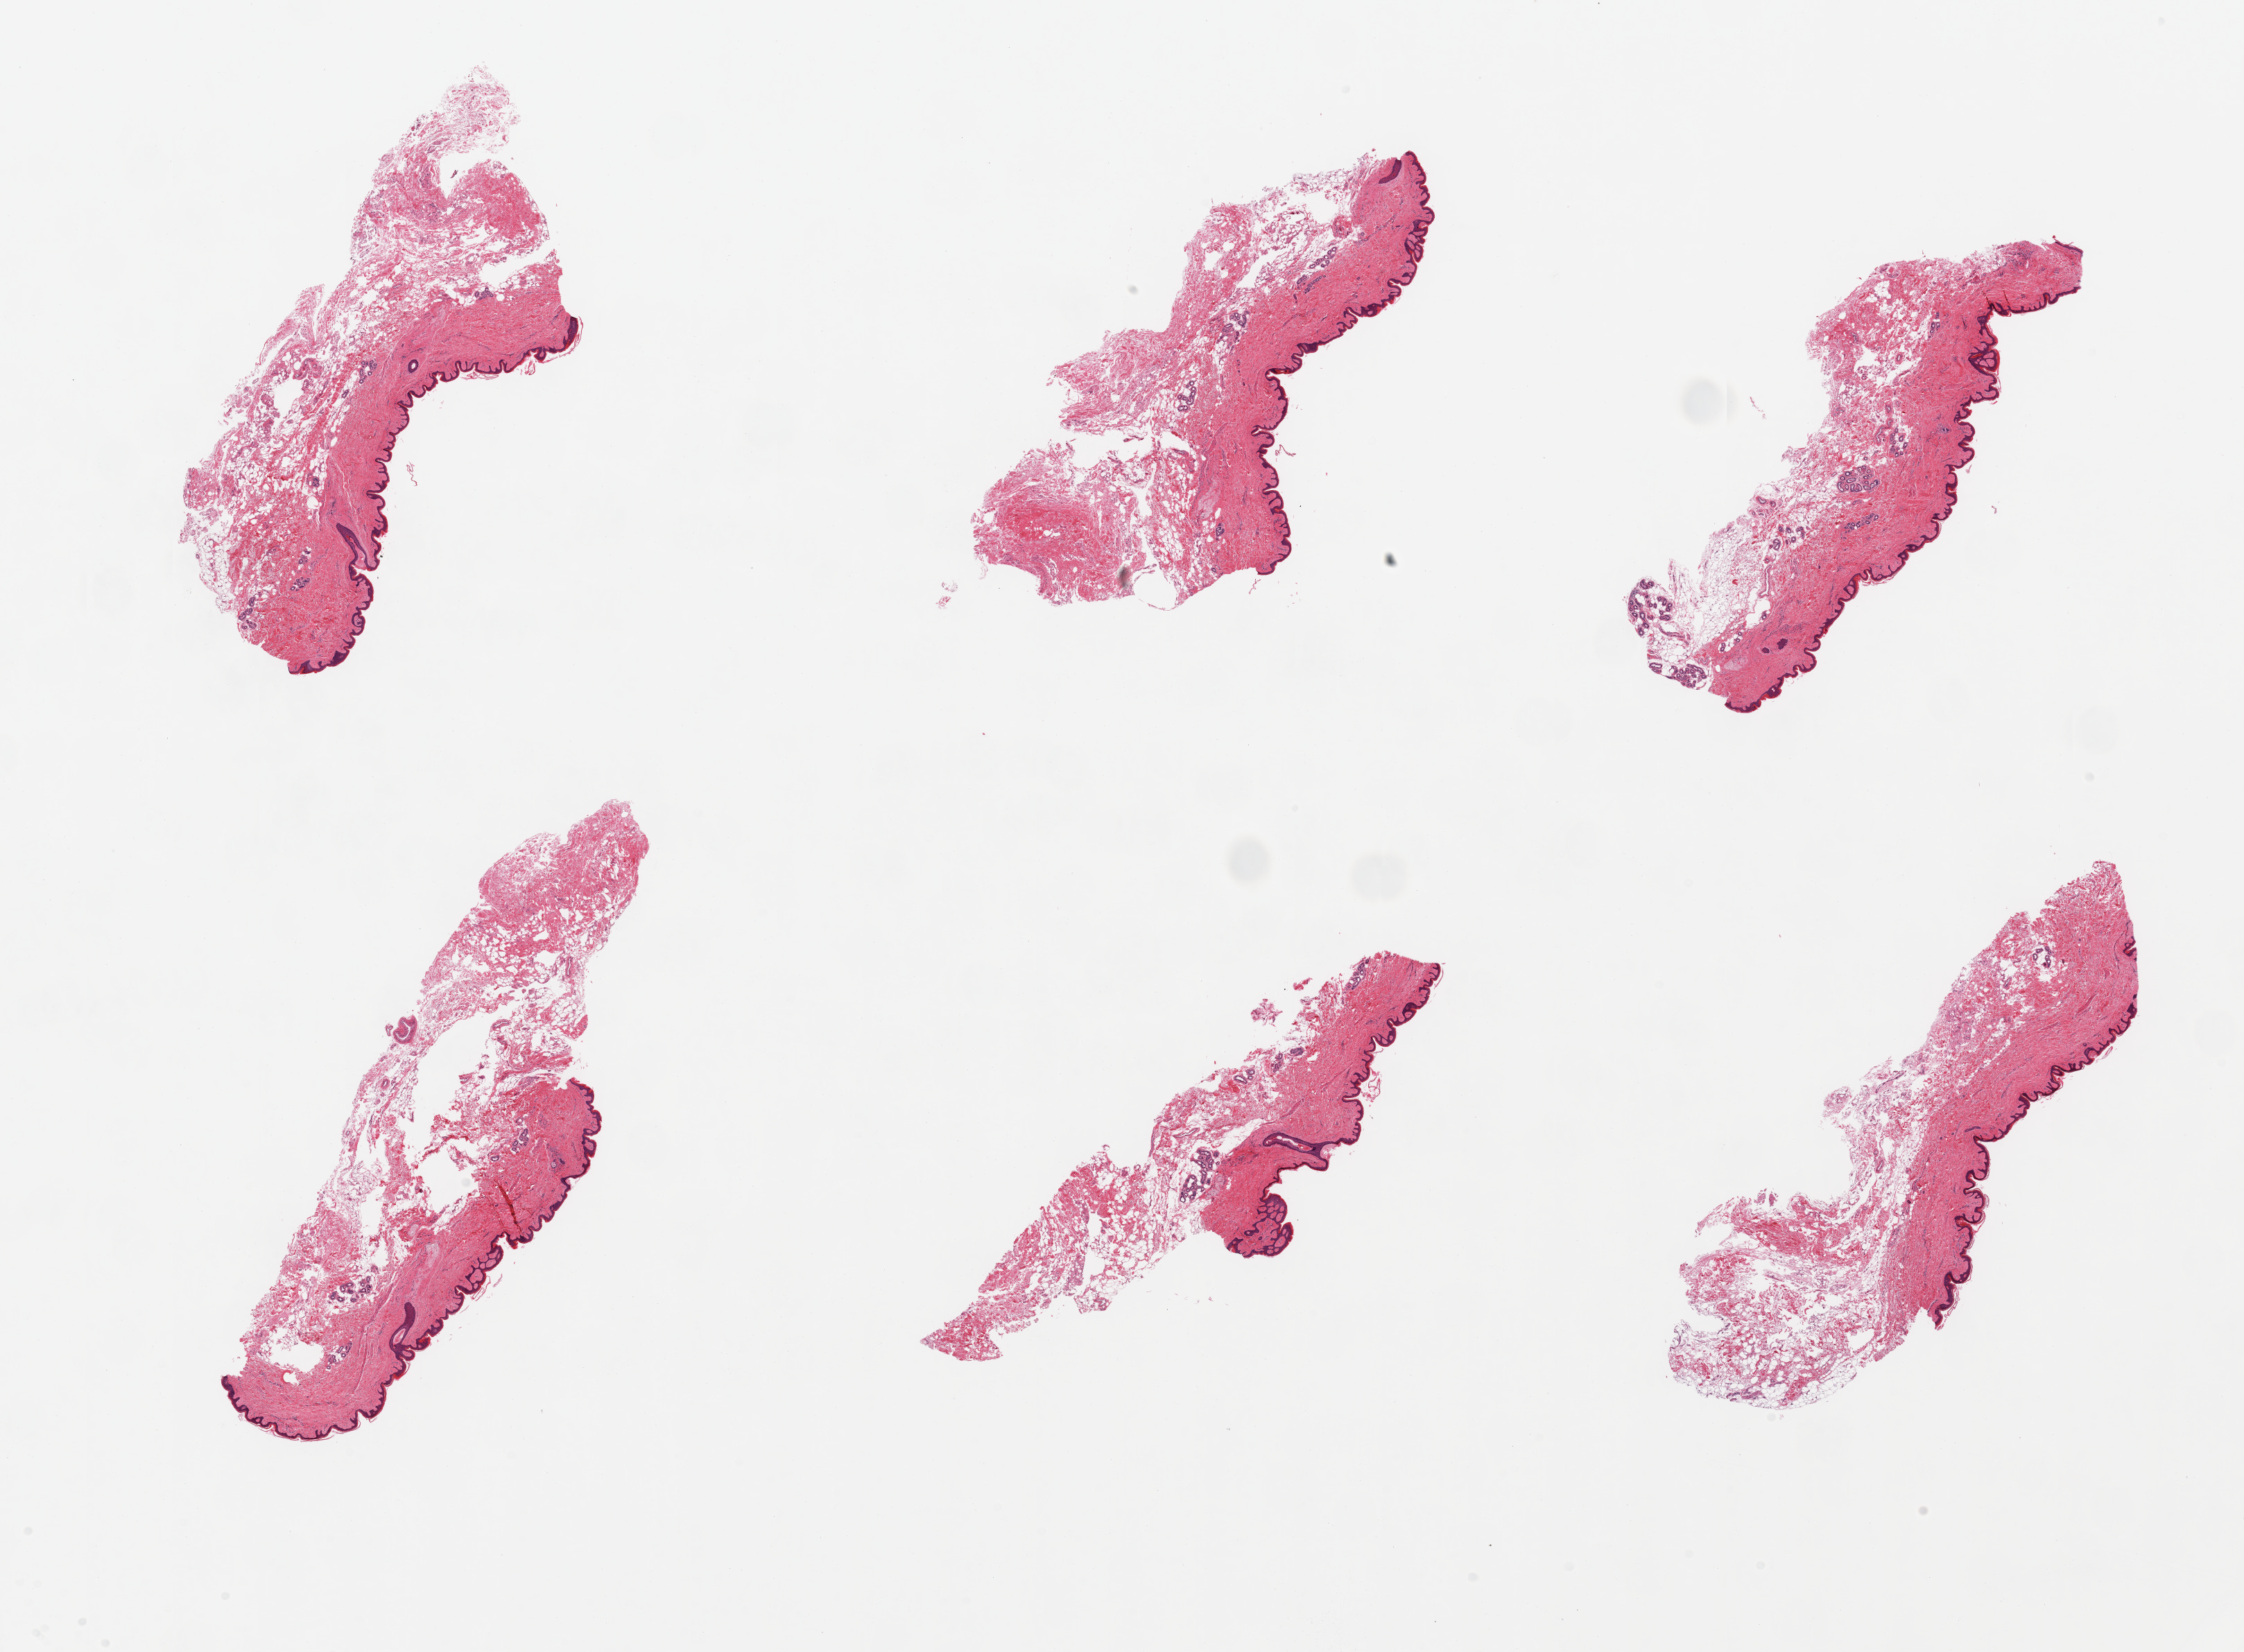
Digitized H&E-stained section, brightfield, whole scanned area (about 25.6 x 18.8 mm) shown as a low-resolution overview, PAXgene-fixed paraffin-embedded (PFPE) section, section of skin of suprapubic region (target tissue), tissue donor sample. Donor sex: female.
Review note (as recorded): 2 pieces; abundant untrimmed subcutaneous fat up to 2 mm thick.